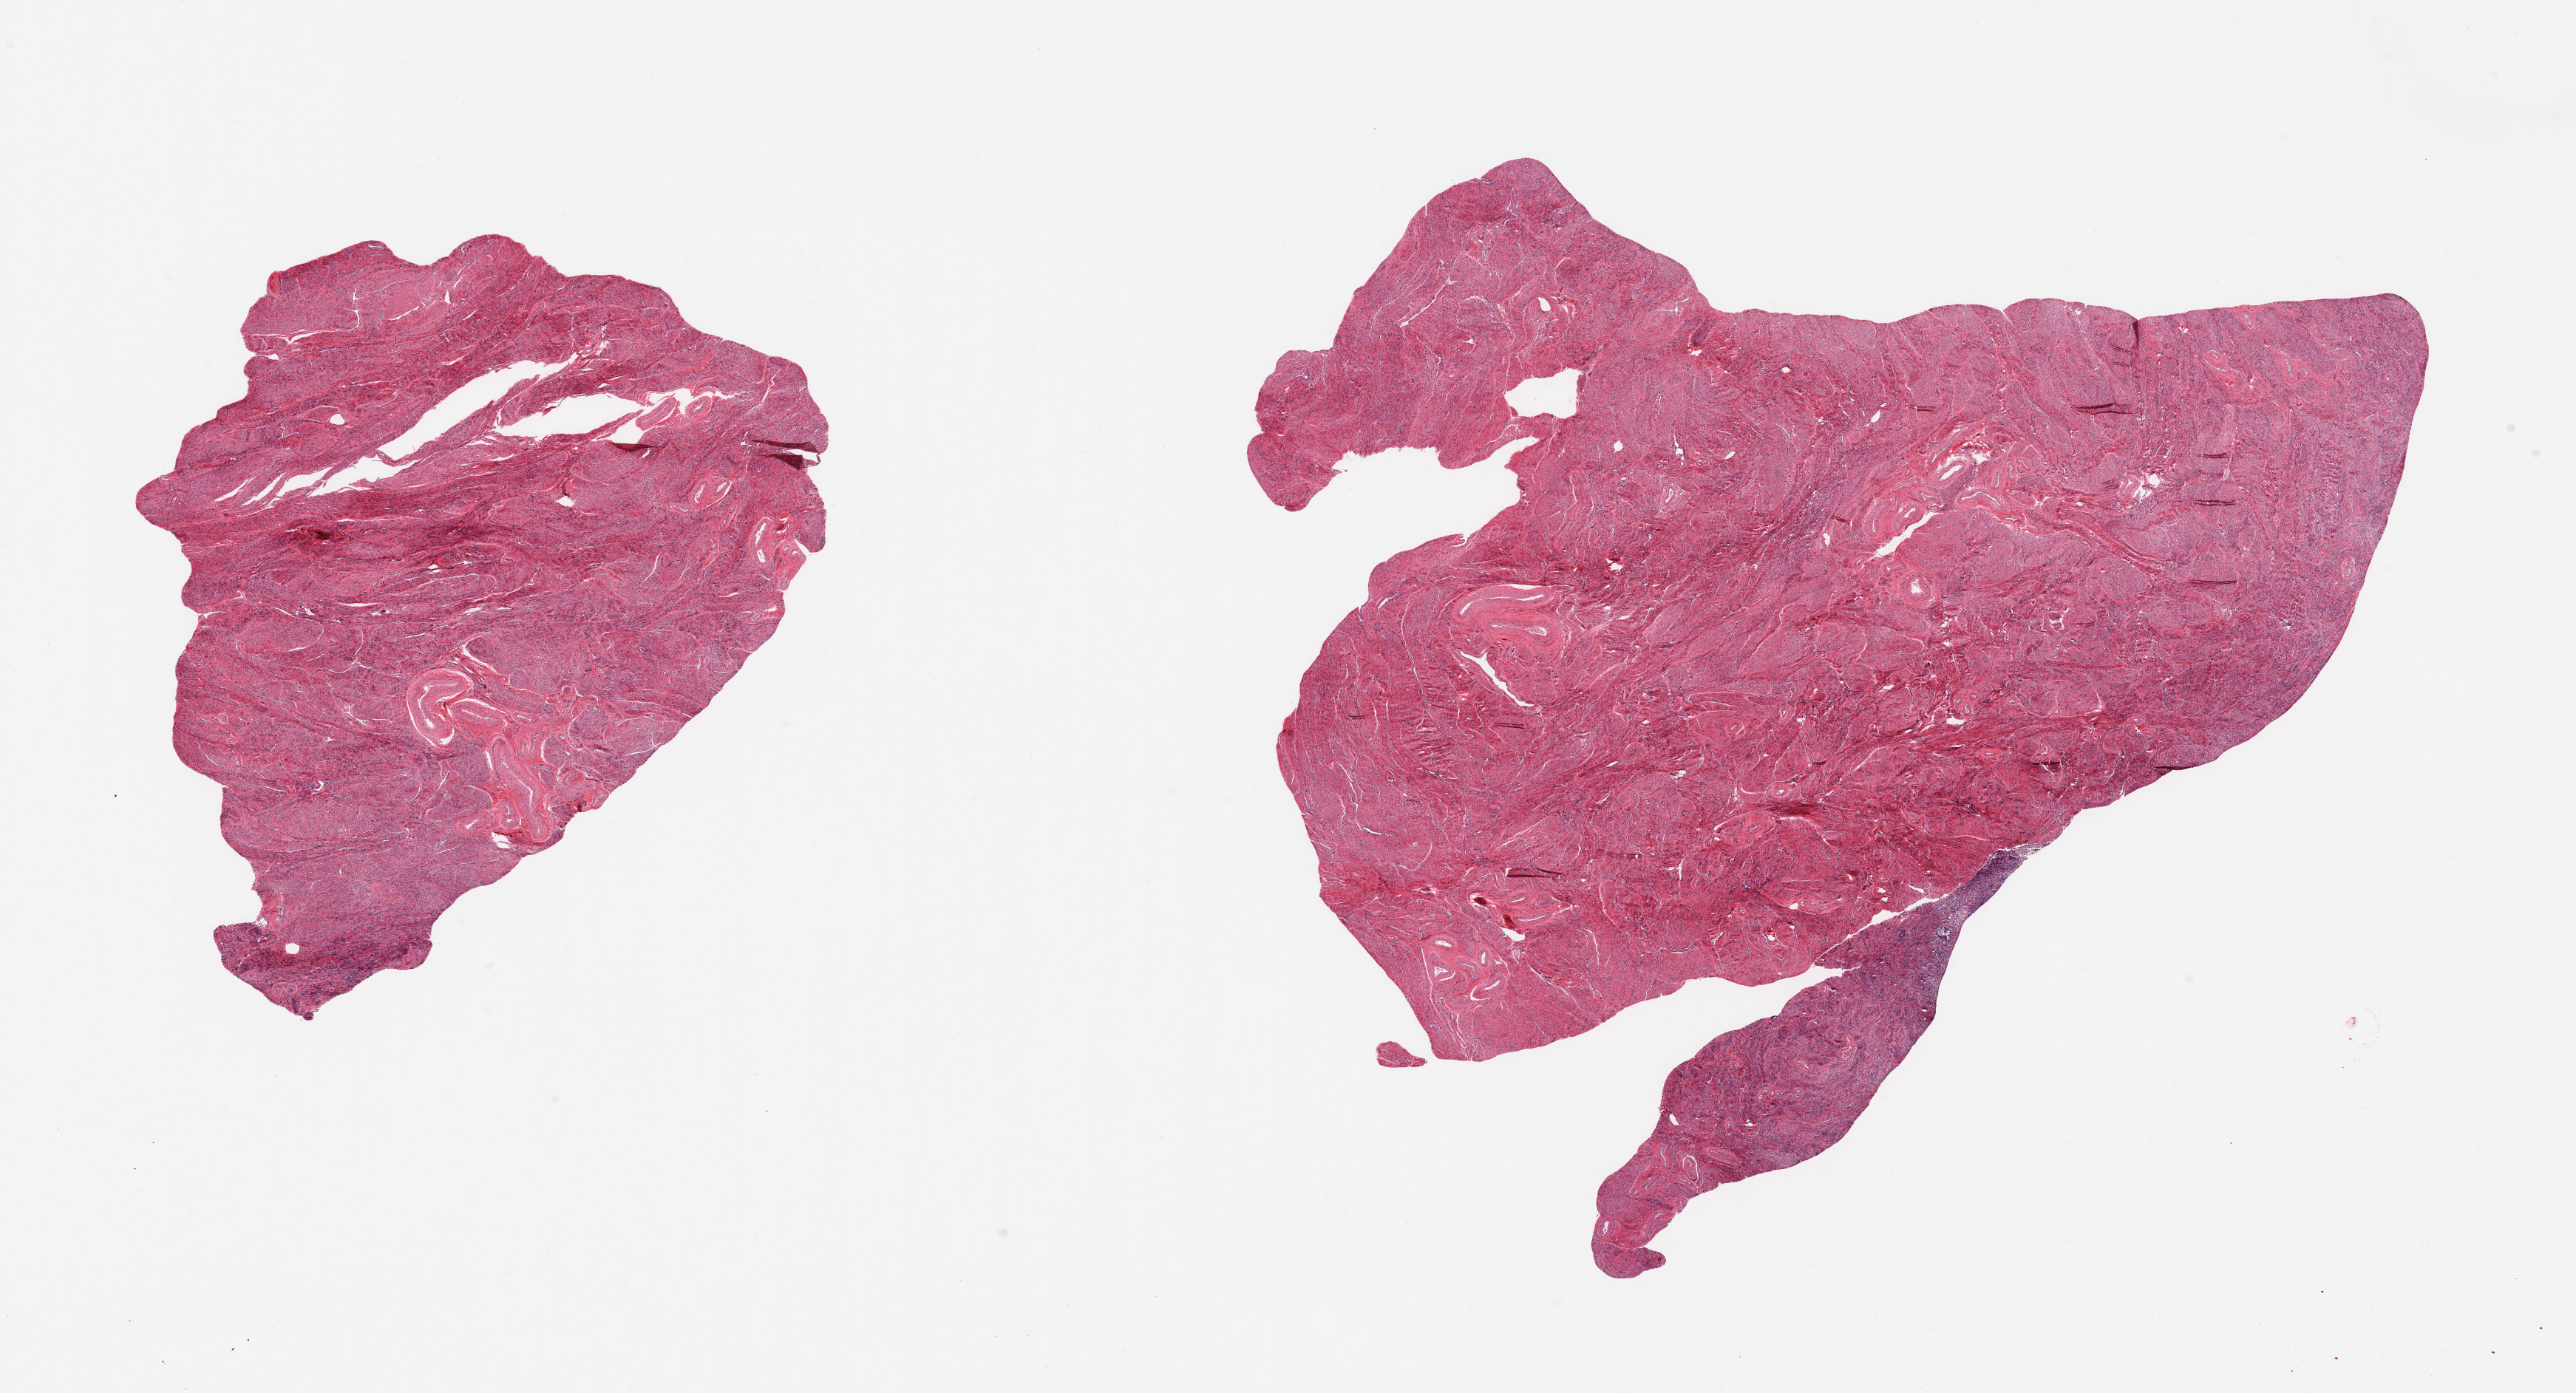
Haematoxylin and eosin whole-slide image, brightfield — shown as a low-resolution overview of the whole scanned area (about 27.6 x 14.9 mm, from a 20x scan); PAXgene-fixed paraffin-embedded (PFPE) section; target tissue: uterus; tissue donor sample. Donor: female.
Pathologist's review note for this sample: 2 pieces; small focus of autolyzed, atrophic endometrium; remainder is preserved myometrium.